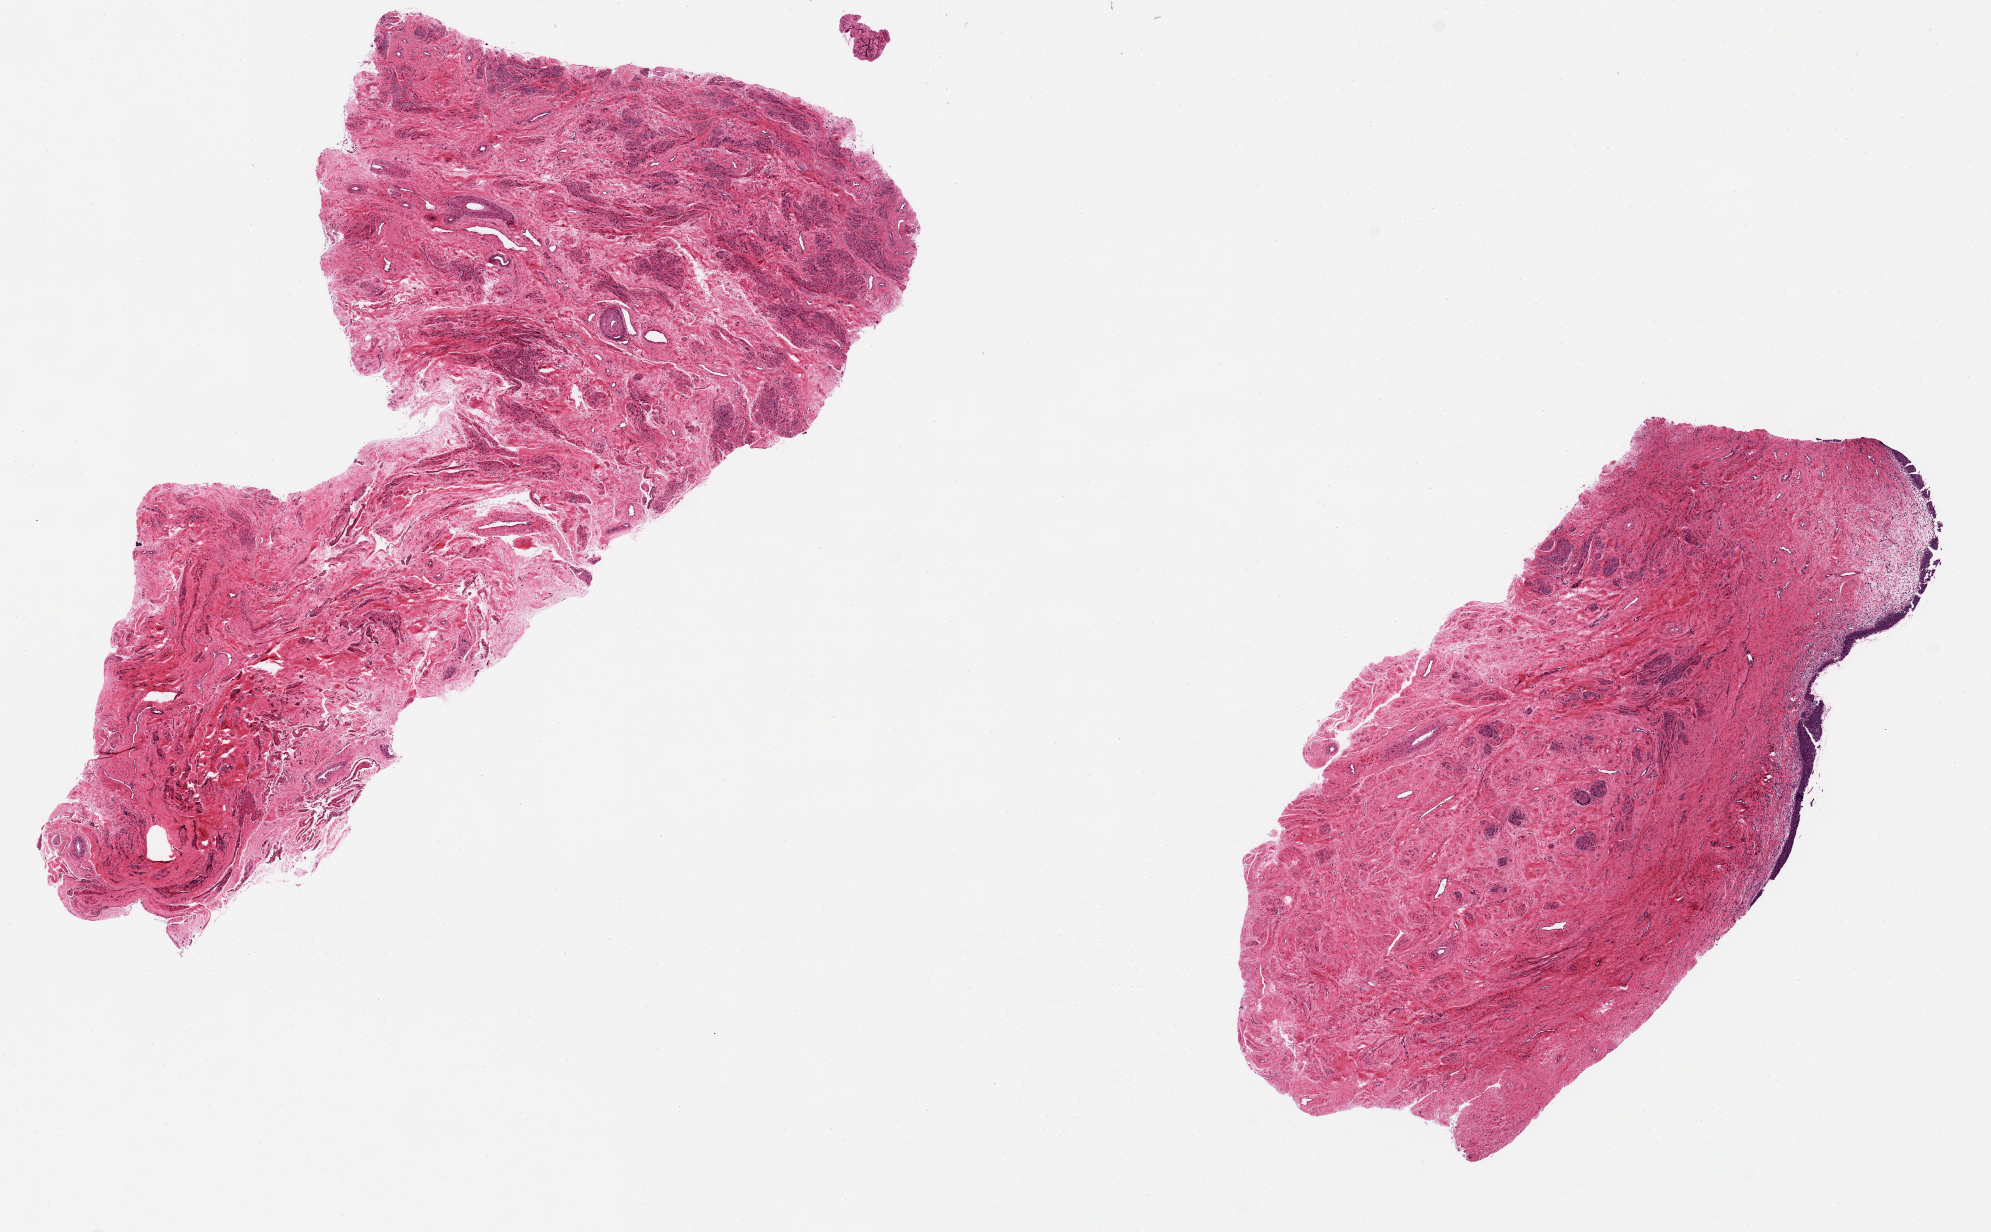
Whole-slide image, H&E stain — low-resolution overview of the scanned area, about 15.8 x 9.7 mm (slide scanned at 20x), PAXgene-fixed, paraffin-embedded tissue, section of exocervix (target tissue), donor tissue sample.
- pathologist's review note for this sample: High grade dysplasia in one piece with epithelium, partly sloughed